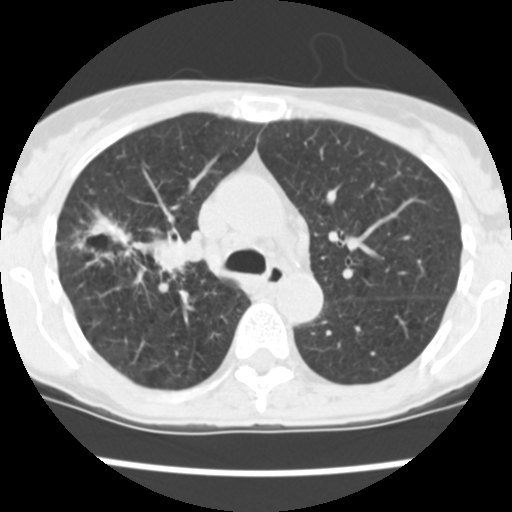
Low-dose screening chest CT, one axial slice. Position 165 of 252 along the scan axis. Reconstruction kernel STANDARD. Lung window (W 1500 / L -600 HU). 2.5 mm slice thickness. 512 × 512 image matrix.
Outlined on this slice (manually delineated by an expert):
- lesion 2 (tumor, lower lobe of right lung): bounding box [x1, y1, x2, y2] px = [87, 211, 203, 277]